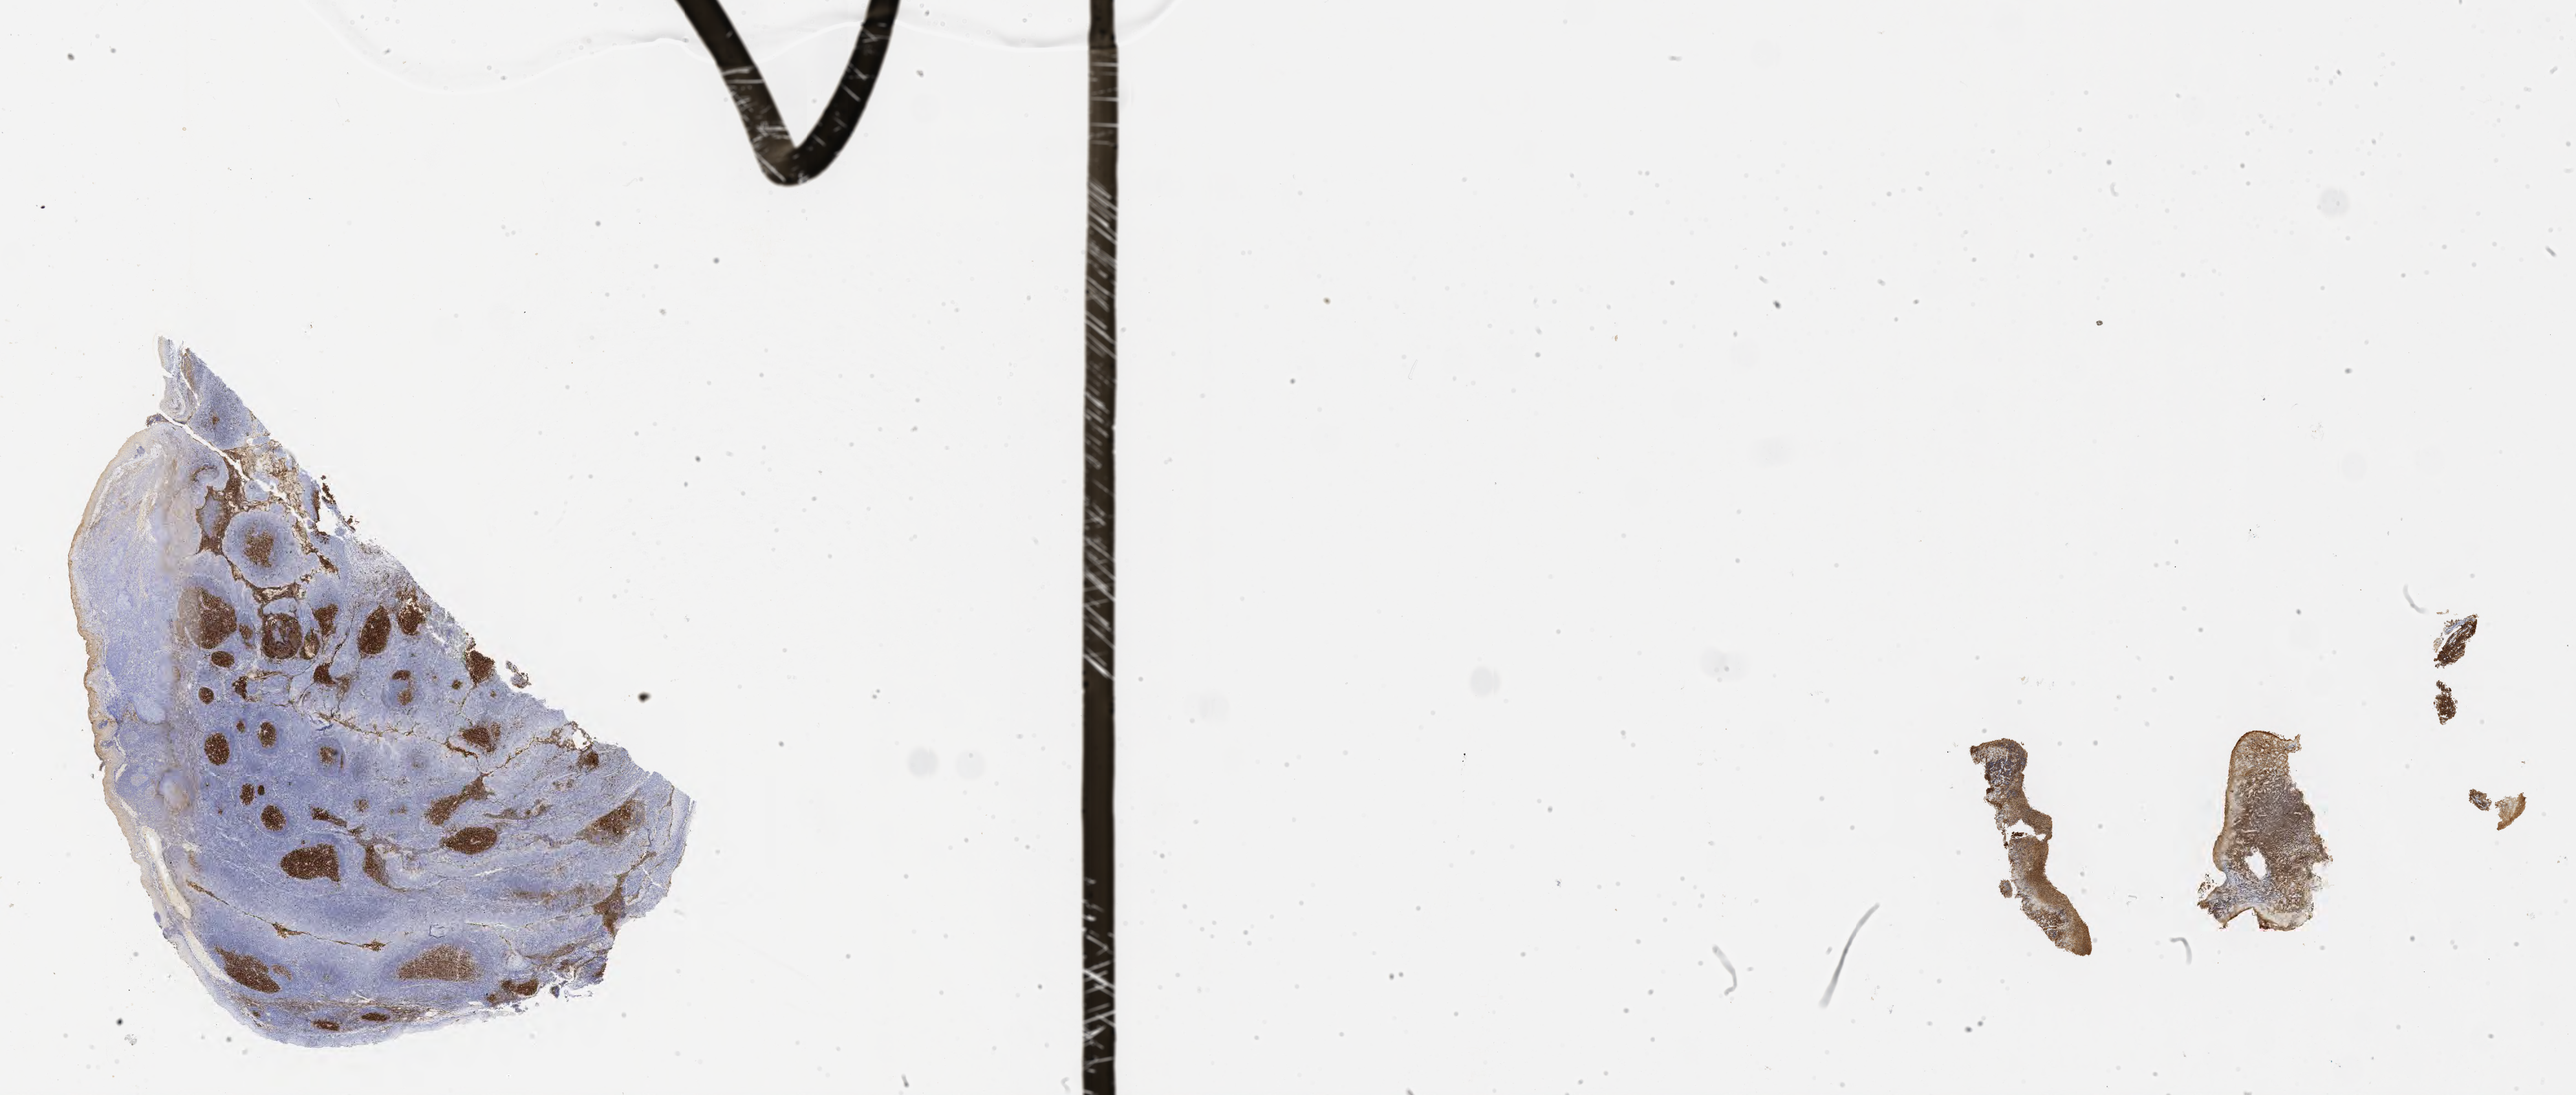
Whole-slide image, immunohistochemical stain for CD10, shown as a low-resolution overview of the whole scanned area (about 32.2 x 13.7 mm). Tumor tissue. Site: colon. Patient male; aged 28.
Diagnosis: Burkitt lymphoma, NOS.